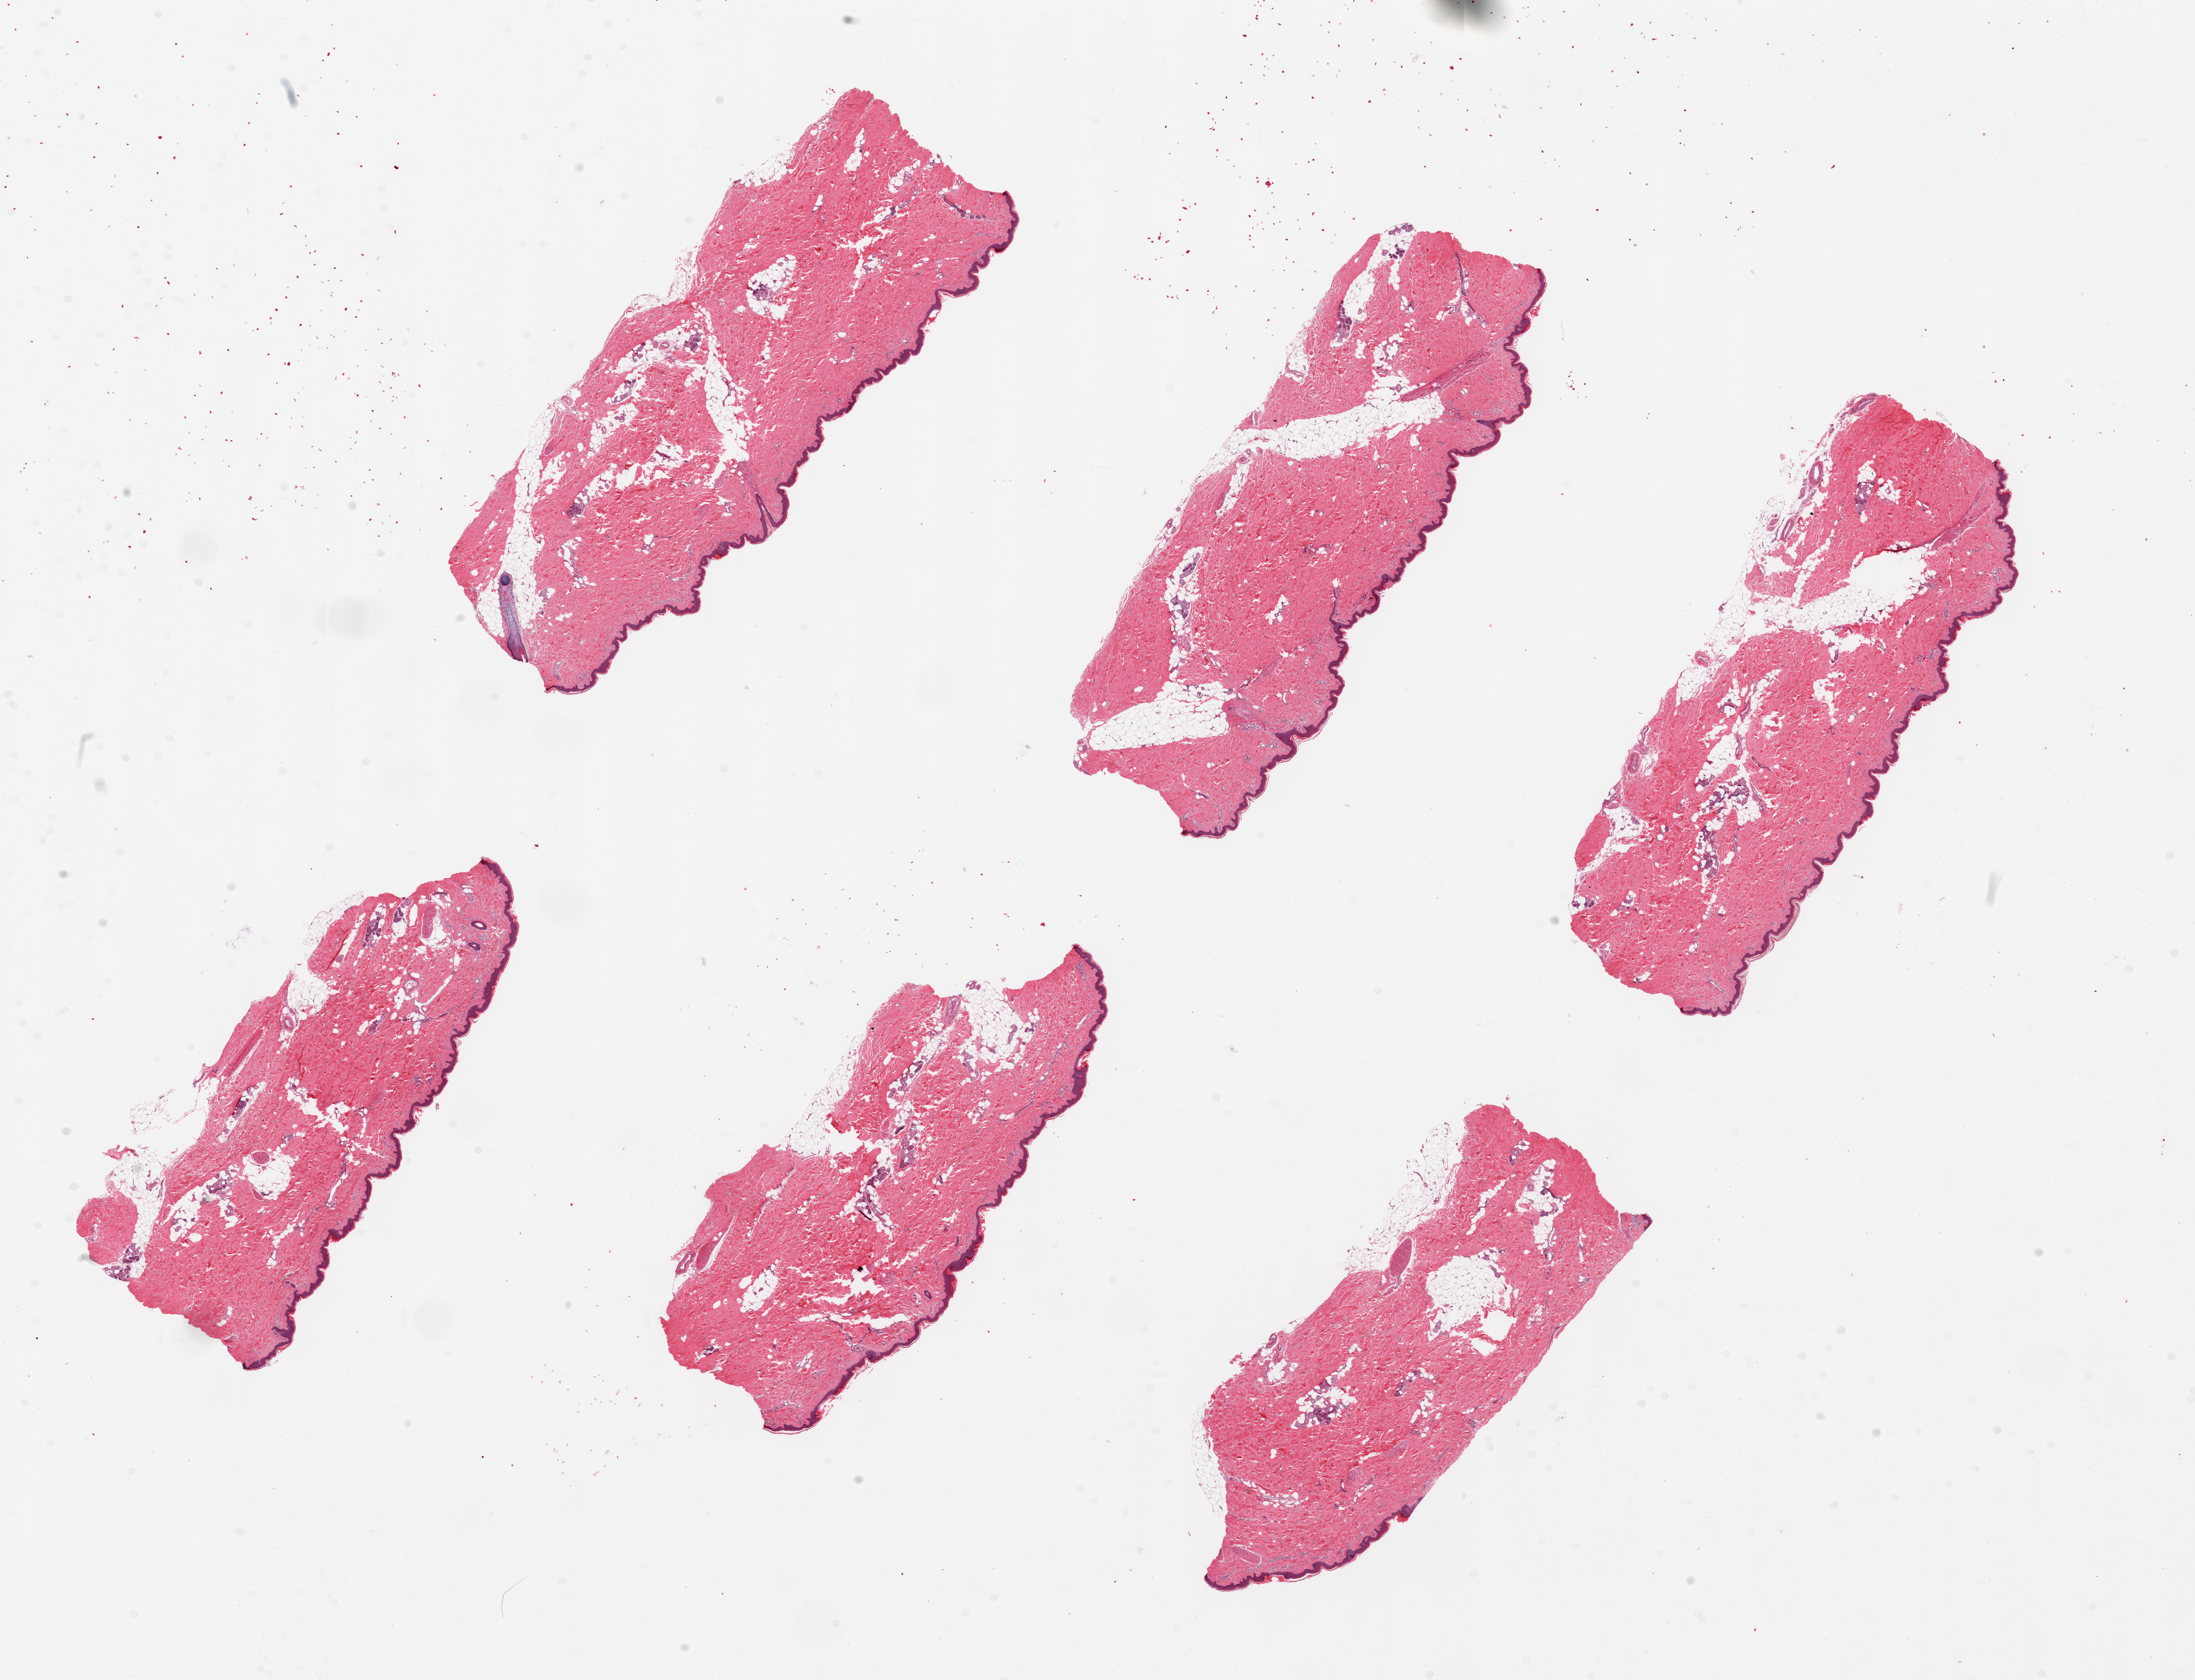
Digitized haematoxylin and eosin-stained section, low-resolution overview of the scanned area, about 26.6 x 20.3 mm (slide scanned at 20x). PAXgene-fixed, paraffin-embedded tissue. Section of skin of lower leg (target tissue). Tissue donor sample.
- review note (as recorded): 6 pieces ~8x3mm; squamous epithelium is 1.5-2% thickness